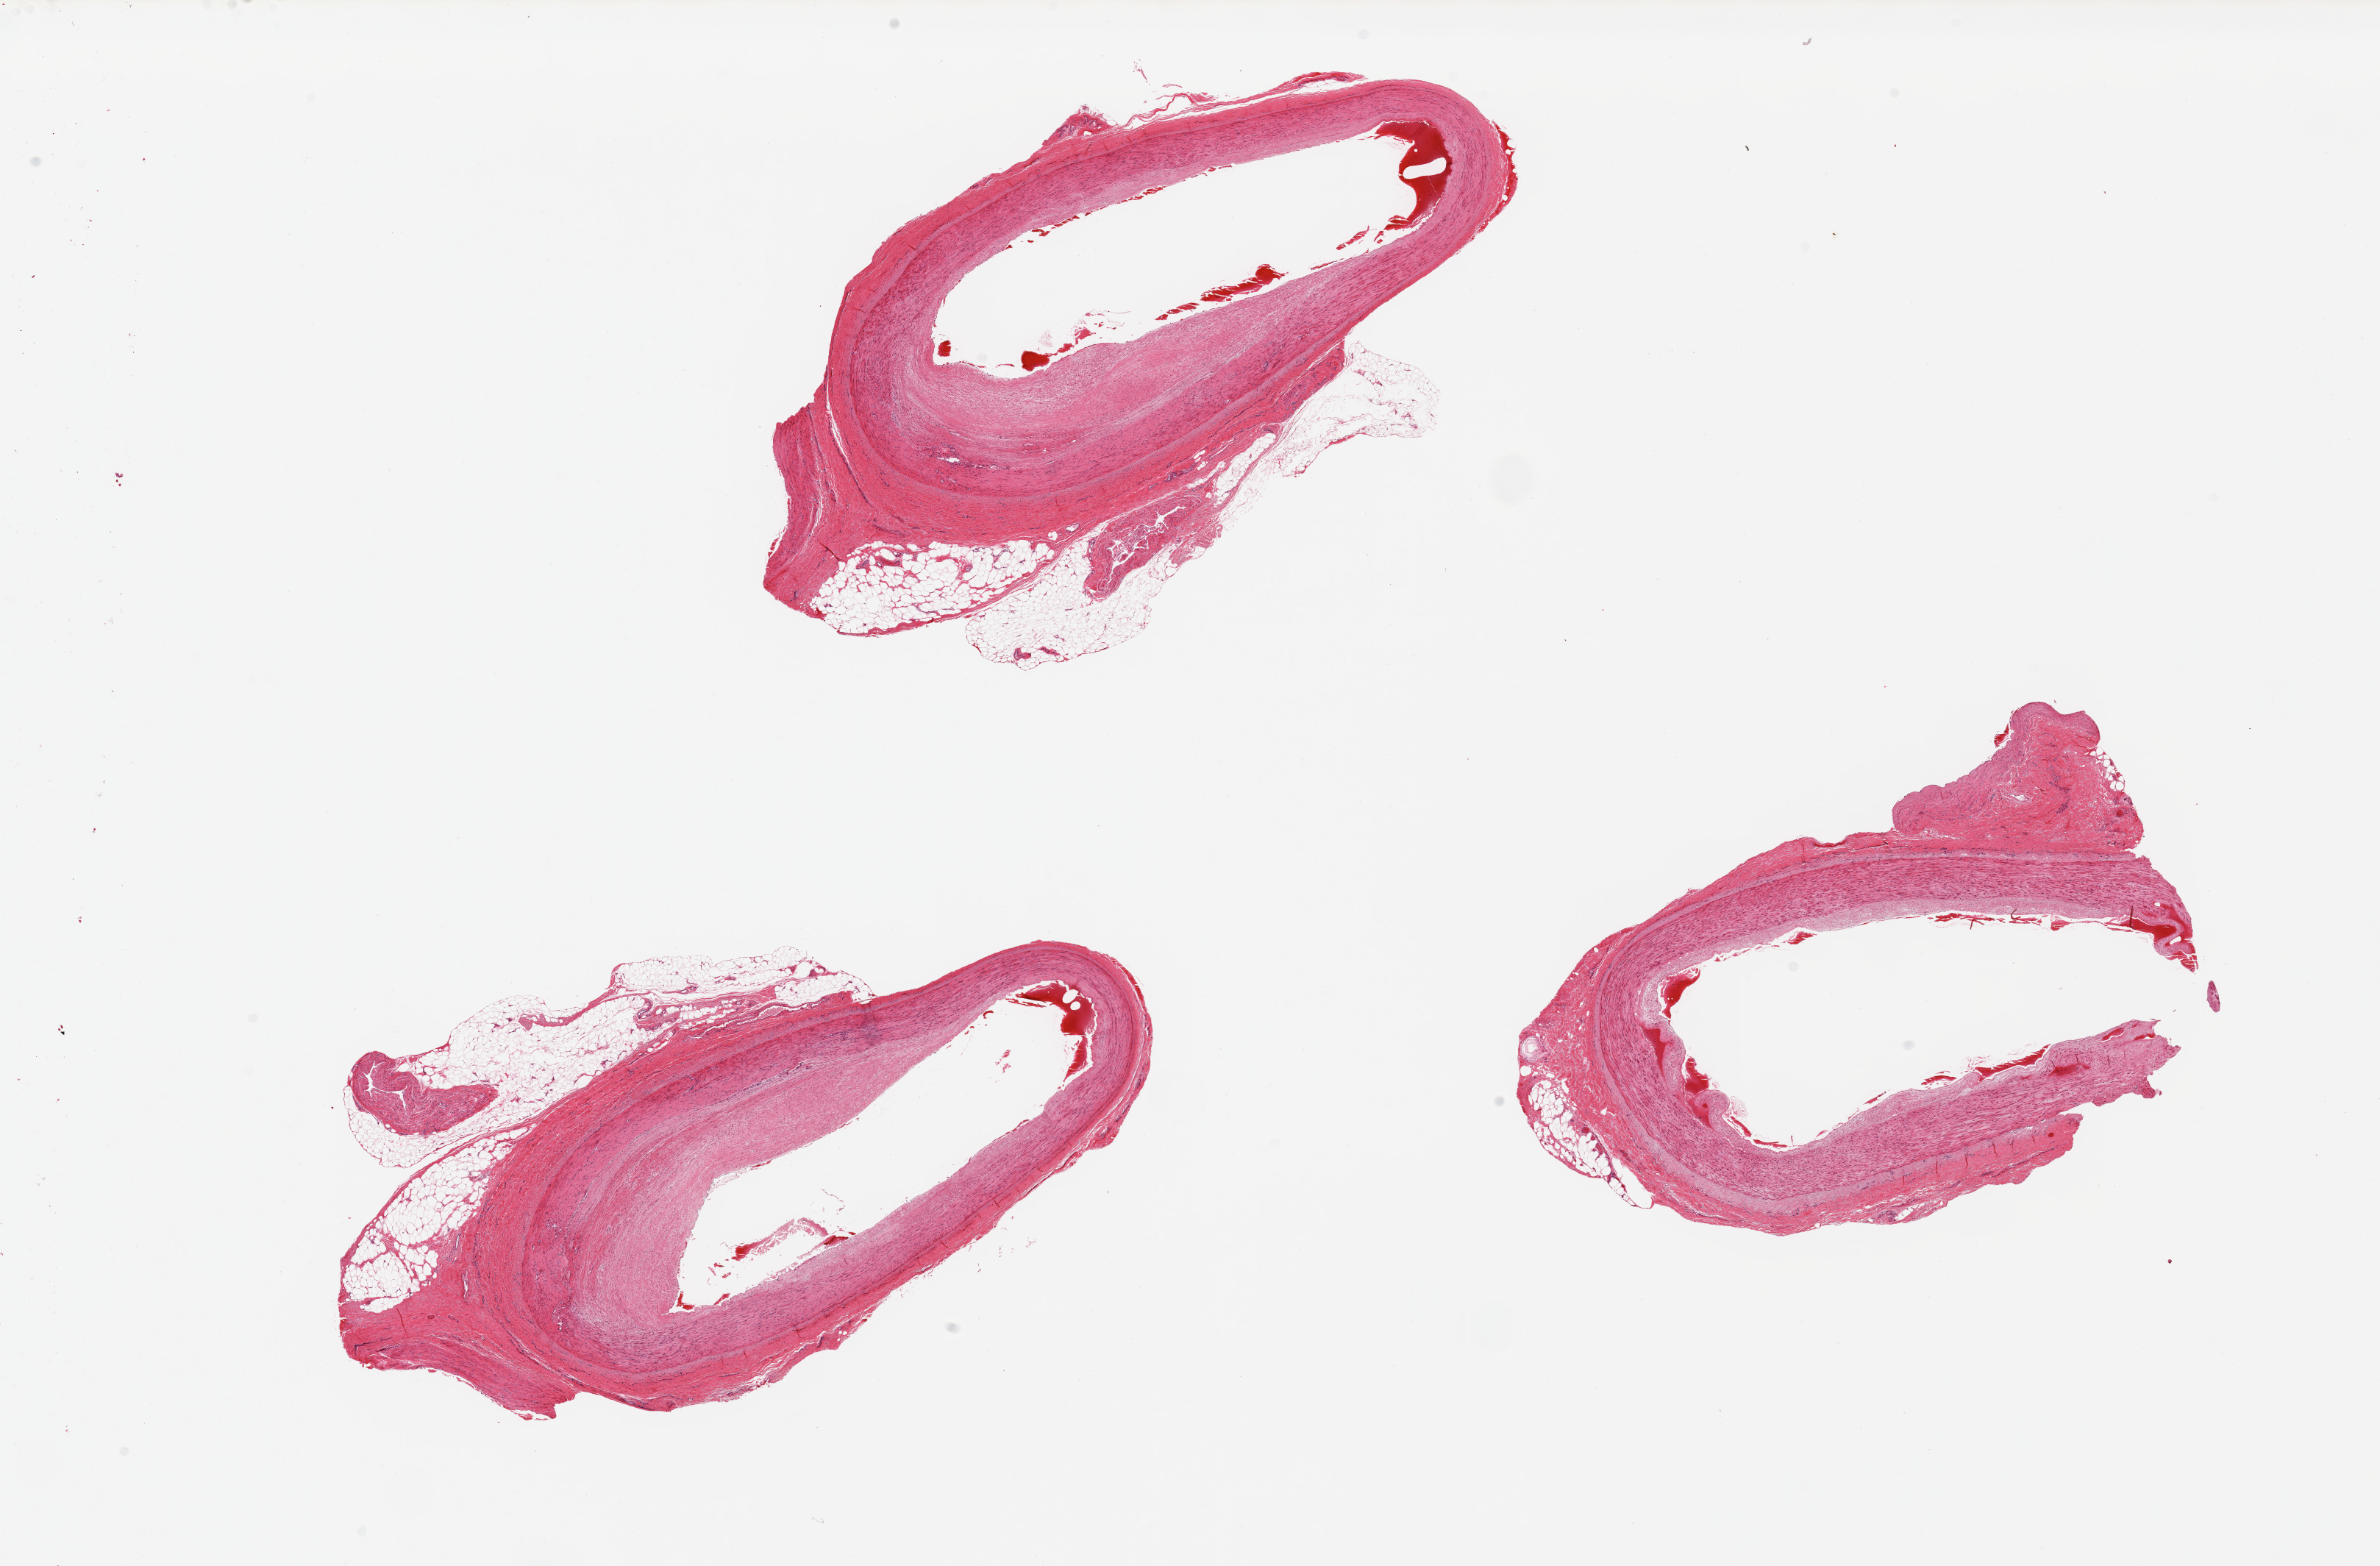
Digitized H&E-stained section — a low-resolution overview of the entire scanned area, about 25.6 x 16.8 mm (acquisition: 20x scan). PAXgene-fixed, paraffin-embedded tissue. Target tissue: tibial artery. Donor tissue sample.
Reviewer comment on this tissue sample: 3 pieces; eccentric fibrous plaques; up to 1 mm external fat.